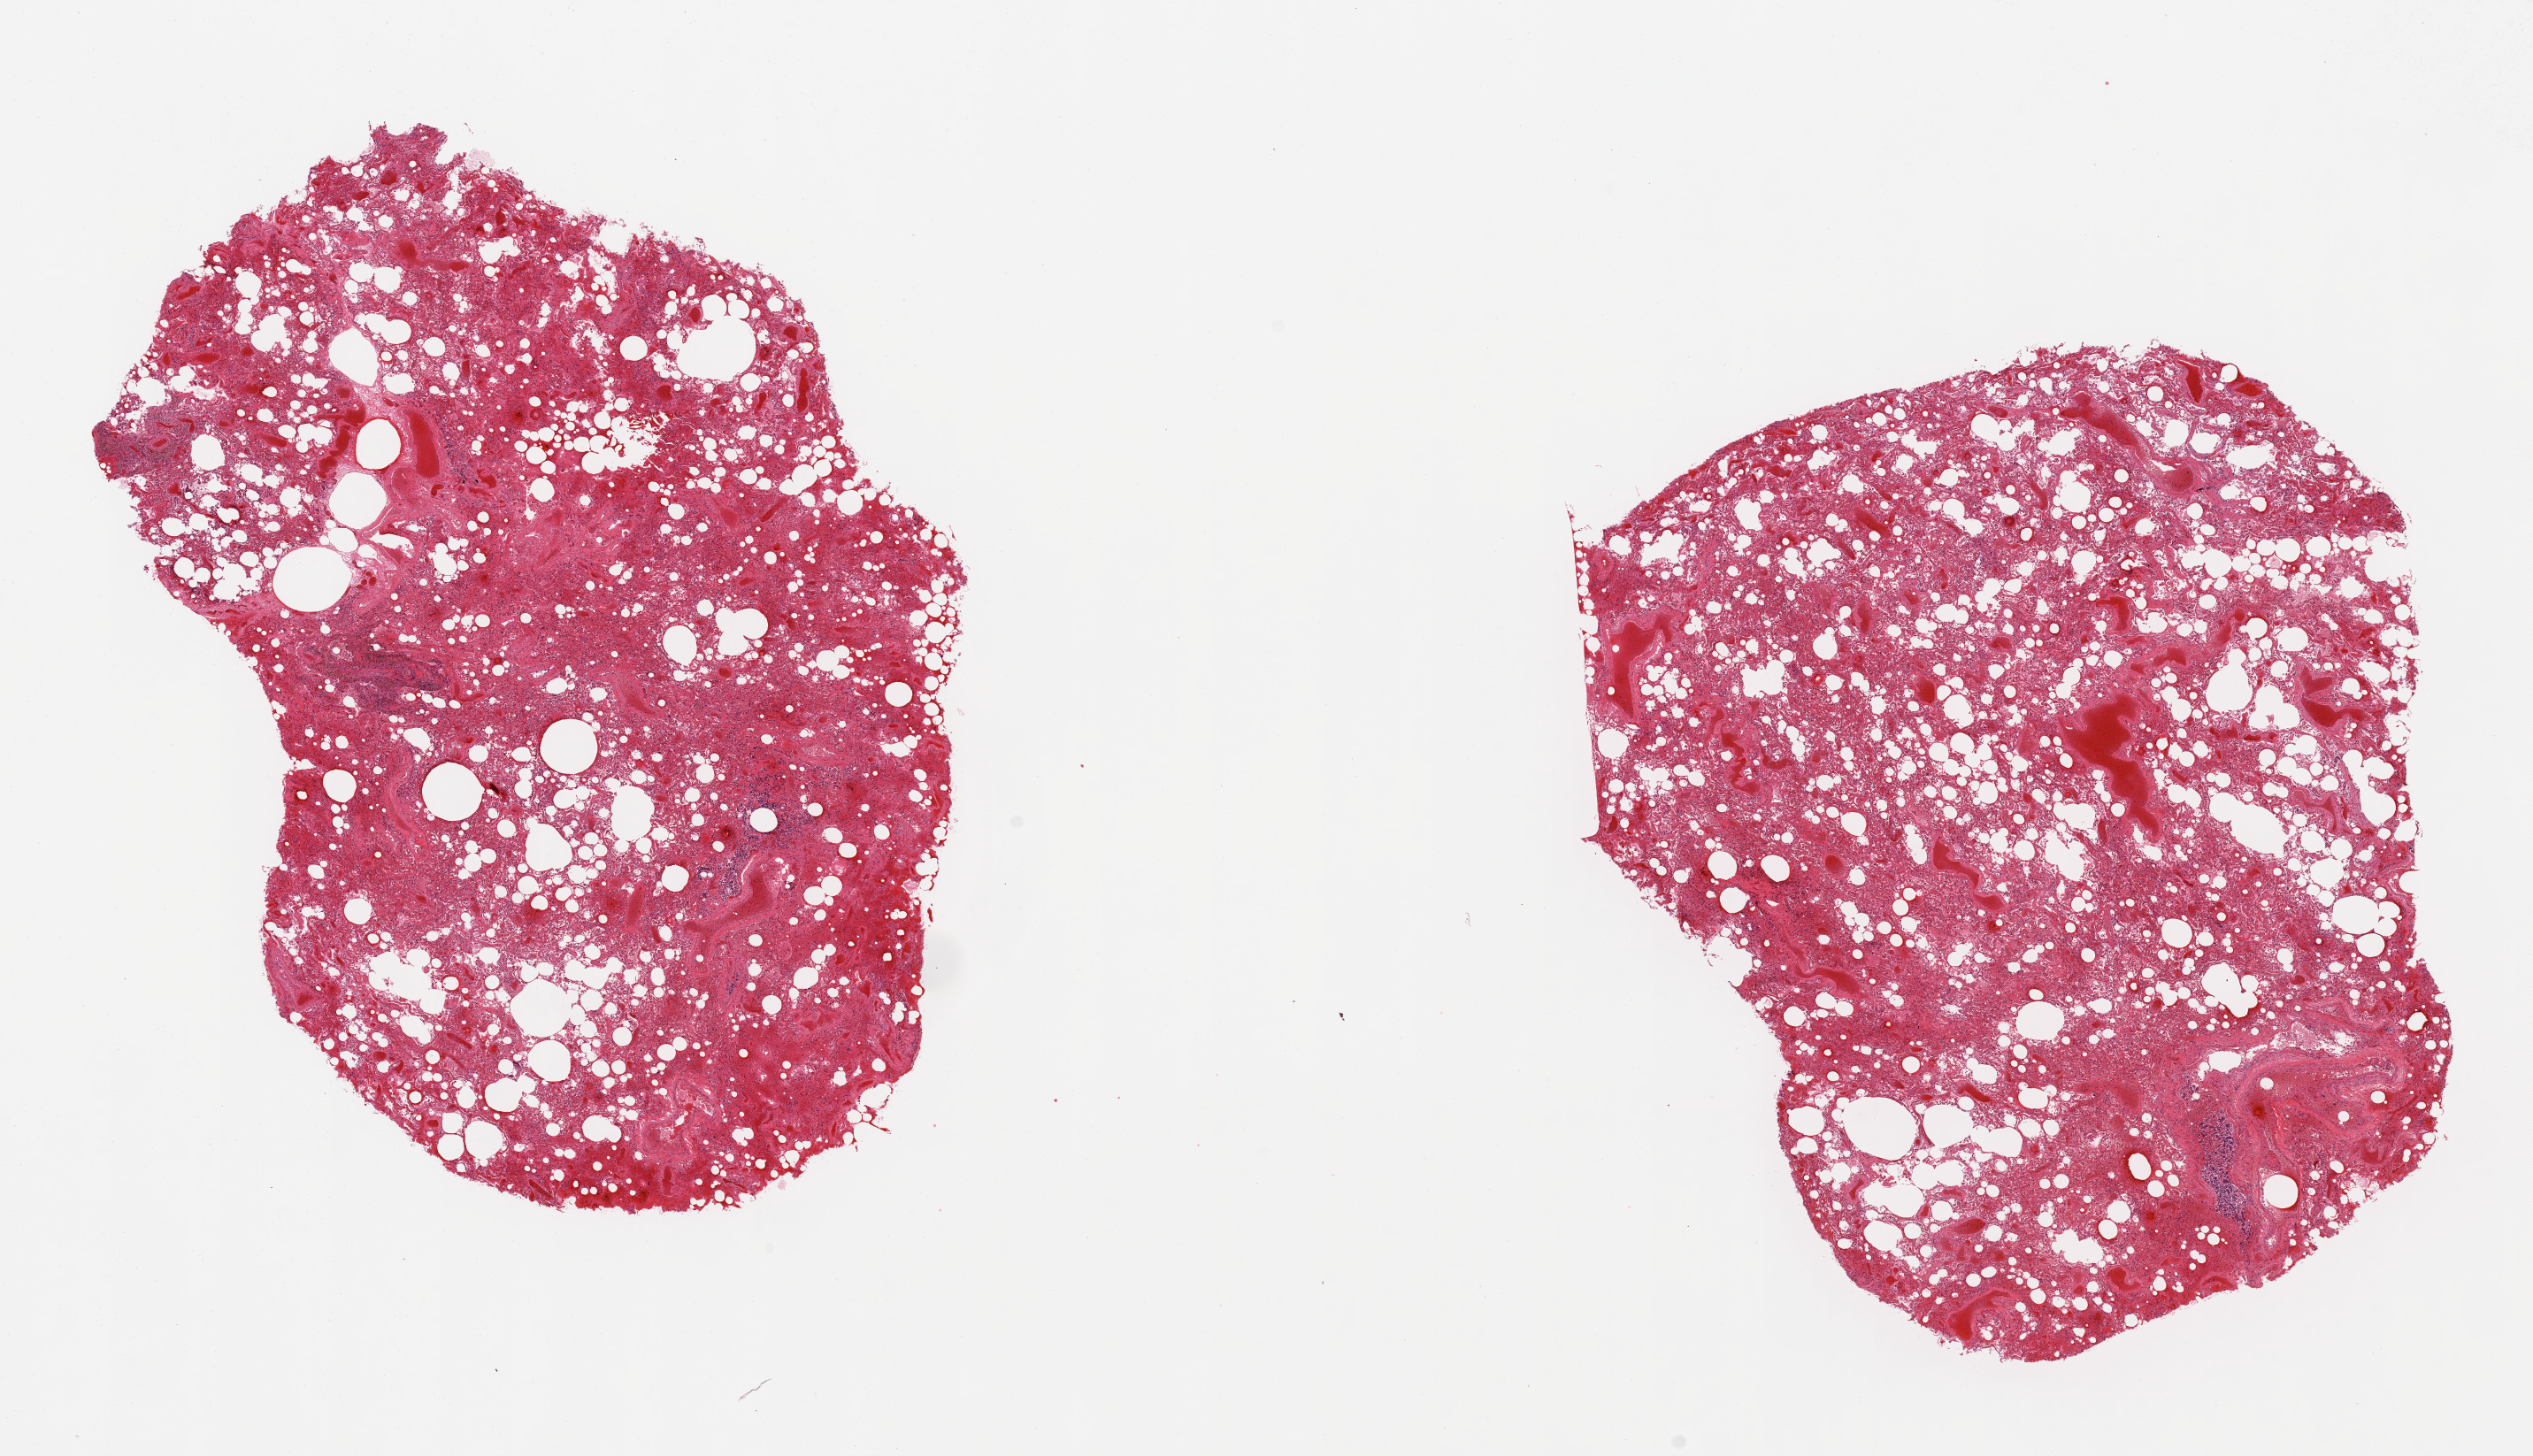
Digitized hematoxylin and eosin (H&E)-stained section, brightfield — shown as a low-resolution overview of the whole scanned area (about 22.6 x 13.0 mm); PAXgene-fixed paraffin-embedded (PFPE) section; section of lung (target tissue); donor tissue sample.
Review note (as recorded): 2 pieces, moderate congestion.